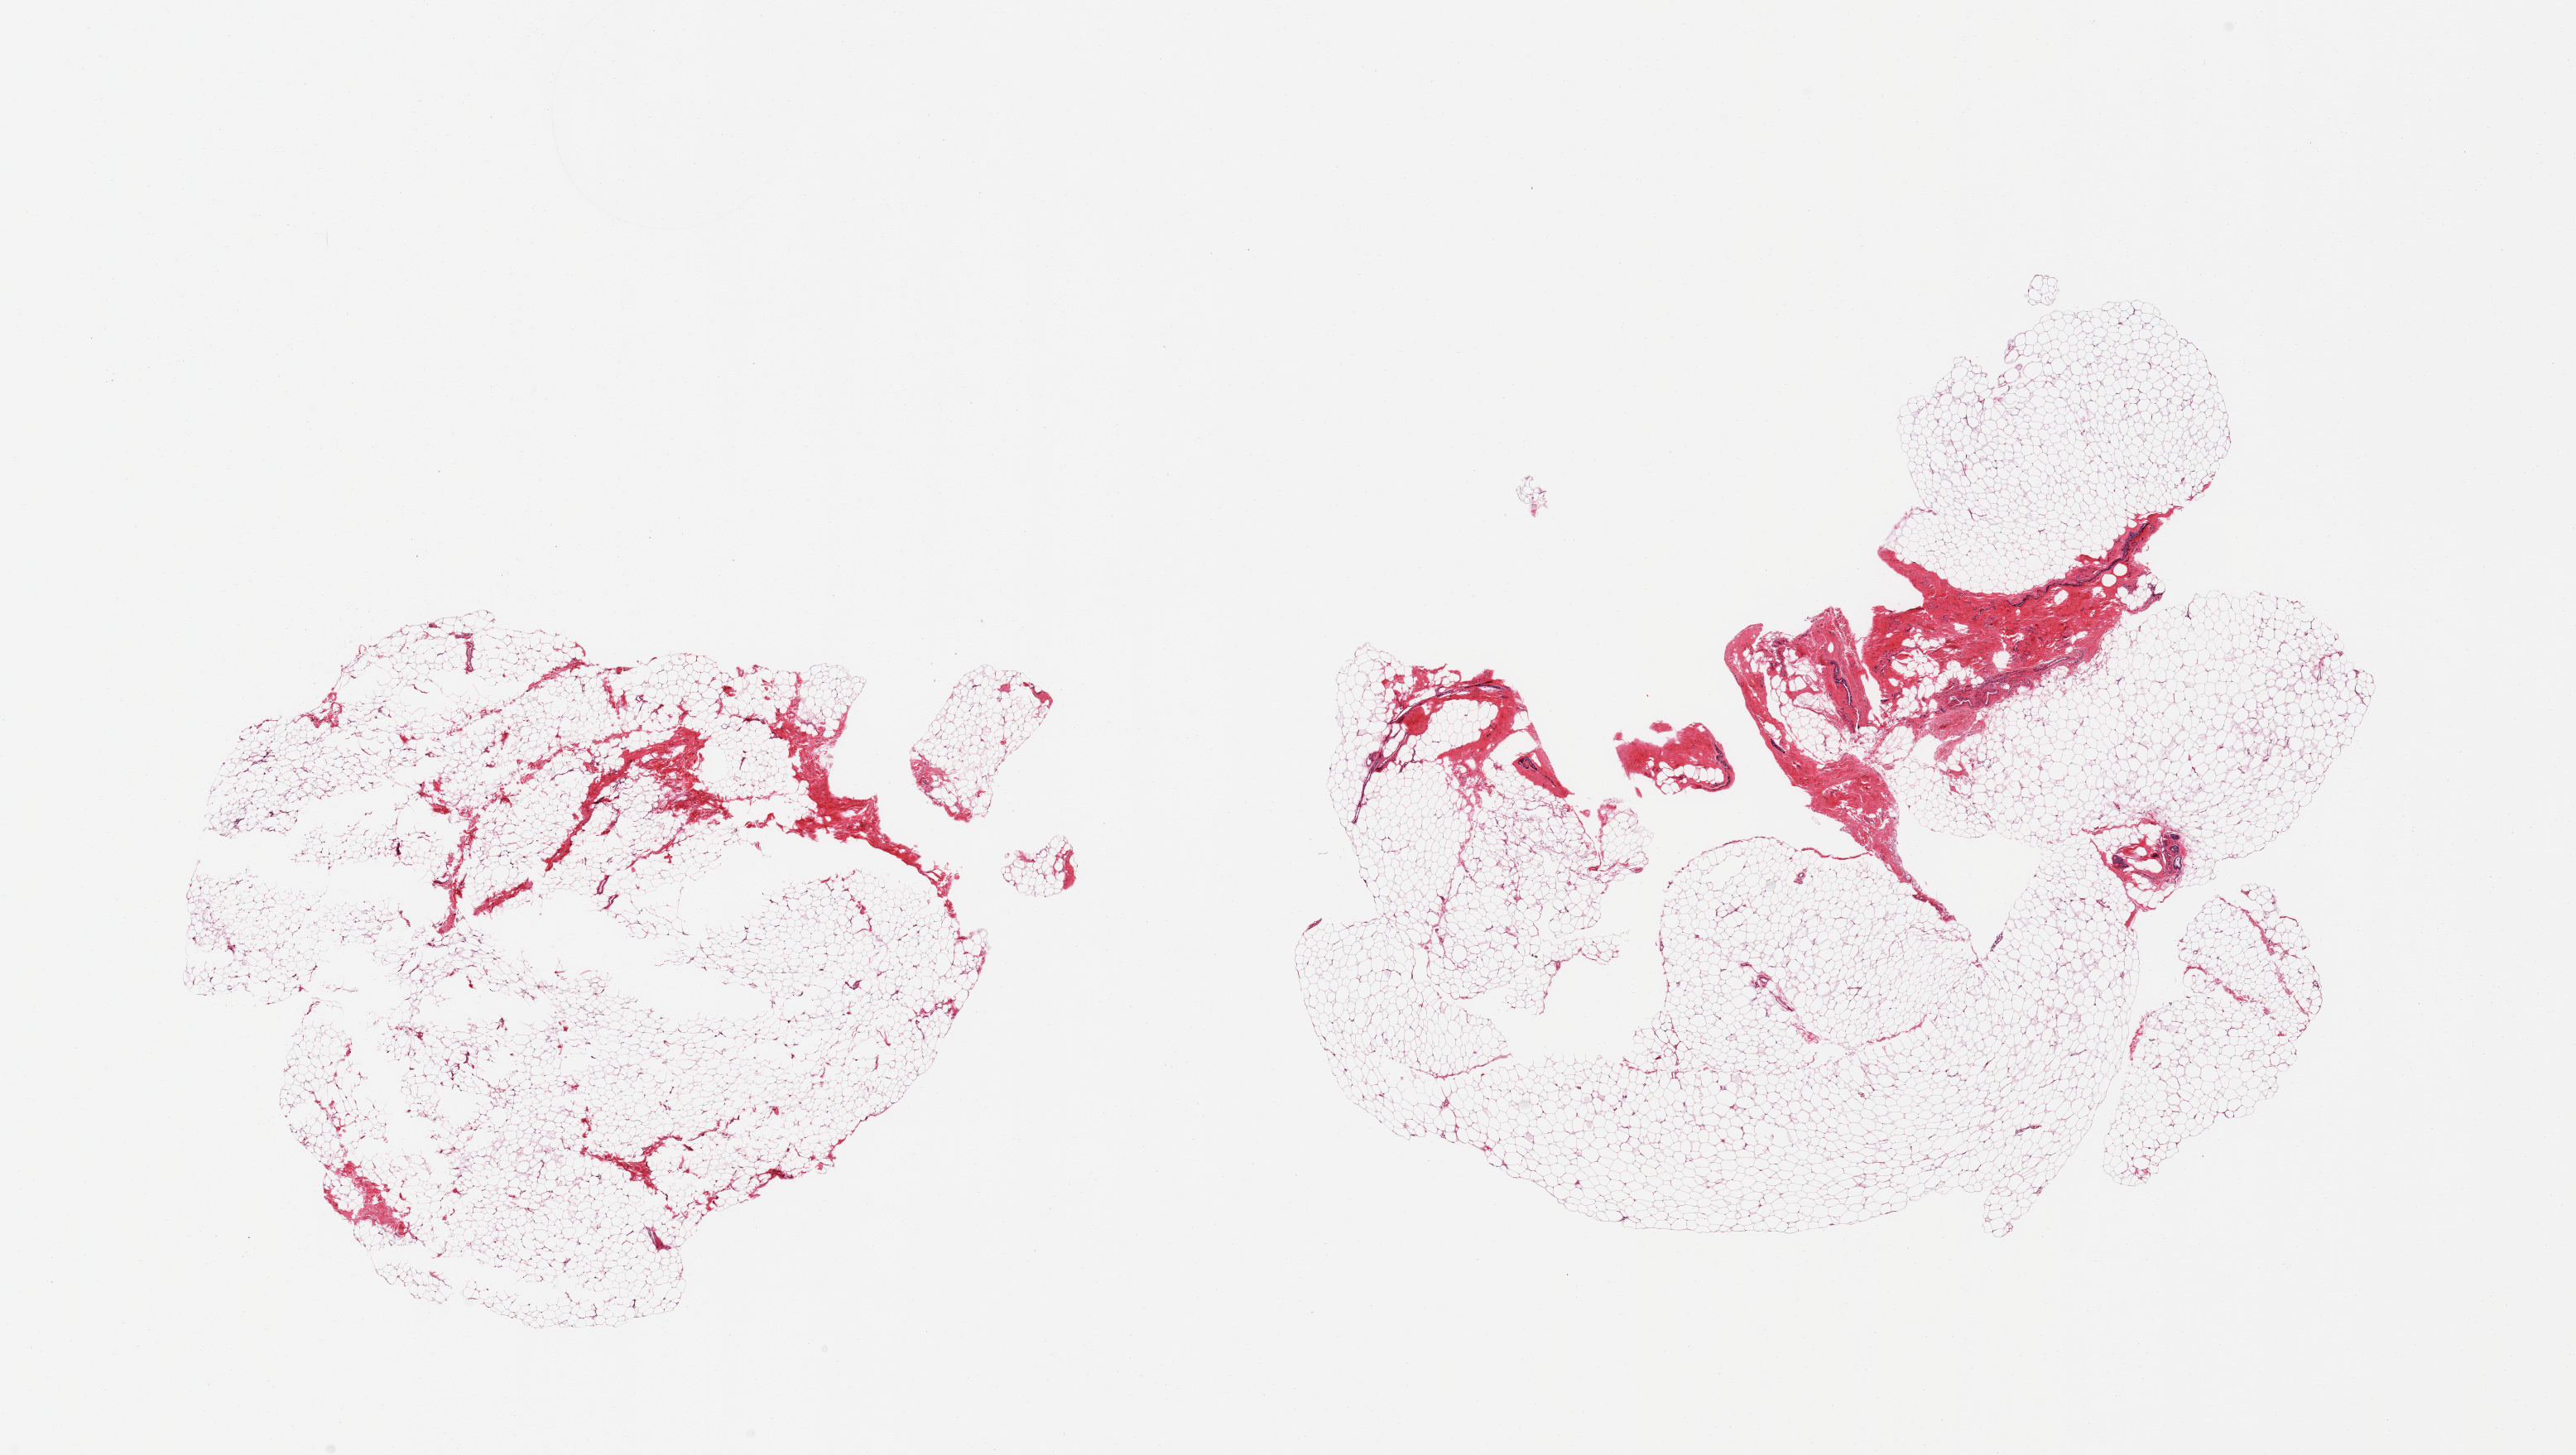
Digitized H&E-stained section, brightfield, shown as a low-resolution overview of the whole scanned area (about 24.6 x 13.9 mm, slide scanned at 20x). PAXgene-fixed, paraffin-embedded tissue. Section of breast (target tissue). Donor tissue sample.
Review note (as recorded): 2 pieces, mainly fibroadipose elements; trace ductal elements.